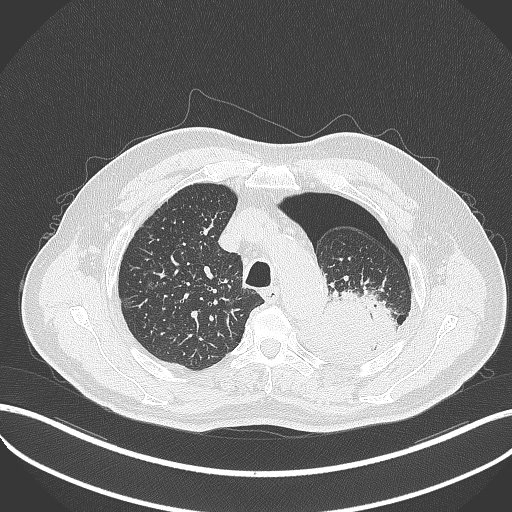
Chest CT, one axial slice; position 394 of 464 along the scan axis; reconstruction kernel B70f; lung window (W 1500 / L -600 HU); 512 × 512 image matrix, field of view 400 × 400 mm. Patient: male, 76 years. Case-level facts recorded for this patient, not image findings: clinical TNM (as recorded): T3 N0 M1b.
Annotated regions visible in this slice (bounding box drawn by a radiologist):
- lung tumour (recorded histology: adenocarcinoma): box from (x=313, y=288) to (x=397, y=361) px